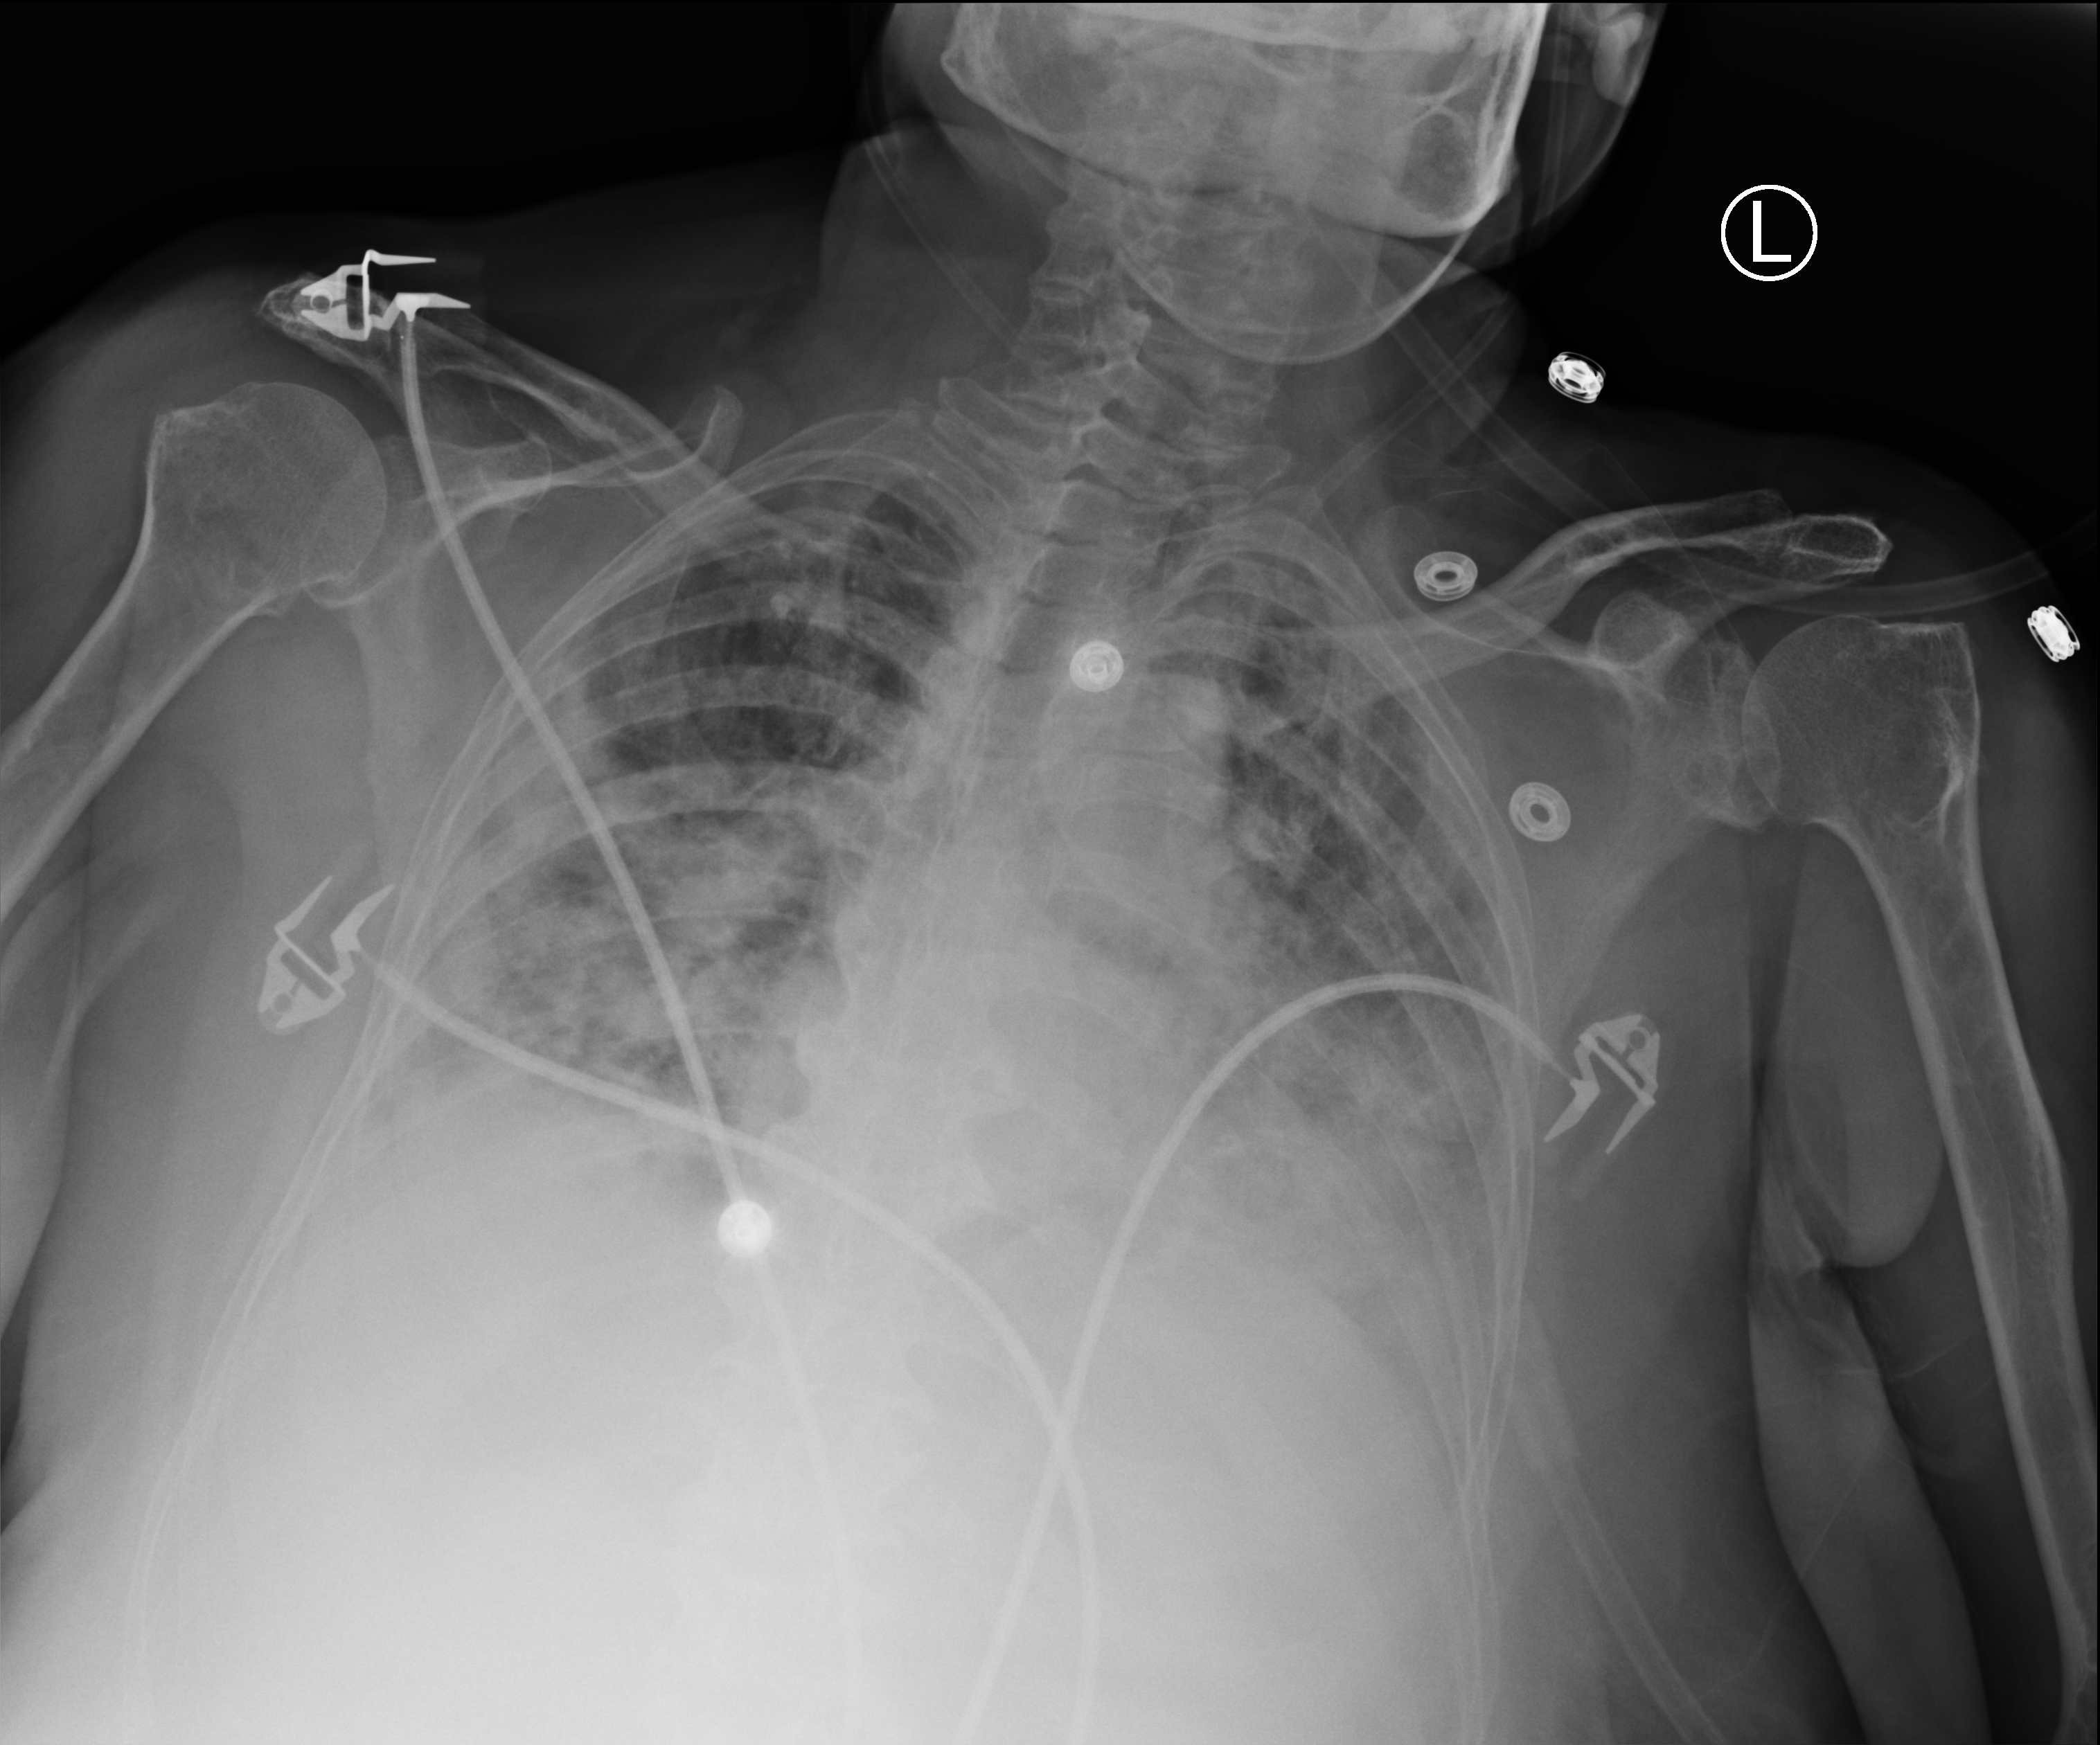
Bedside chest radiograph (computed radiography), anteroposterior (AP) projection. Female patient hospitalised with COVID-19, age 75–90 years.
From the hospital-stay record, not from the radiograph (when in the stay this image was taken is not recorded): mechanically ventilated during this hospital stay: no; COPD (admission record): yes.